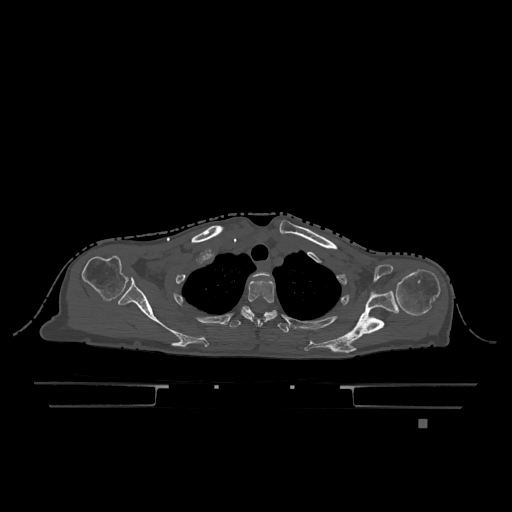
CT including the spine, one axial slice; slice 953 of 1317 in the series (ordered by position); bone window (W 1800 / L 400 HU); 0.5 mm slice thickness; 512 × 512 image matrix, field of view 500 × 500 mm. Female patient, age 74 years. Case-level facts recorded for this patient, not image findings: primary cancer: lung; vertebrae with lytic lesions (as recorded): T1, T4, T5, T6, L4, L5.
Annotated regions visible in this slice (semi-automatically segmented with operator editing):
- T1 vertebra: bounding box <253,272,270,277> (left, top, right, bottom; pixels)
- T2 vertebra: <241,279,278,324>
- T3 vertebra: <229,308,289,333>
- T6 vertebra: <242,306,277,317>